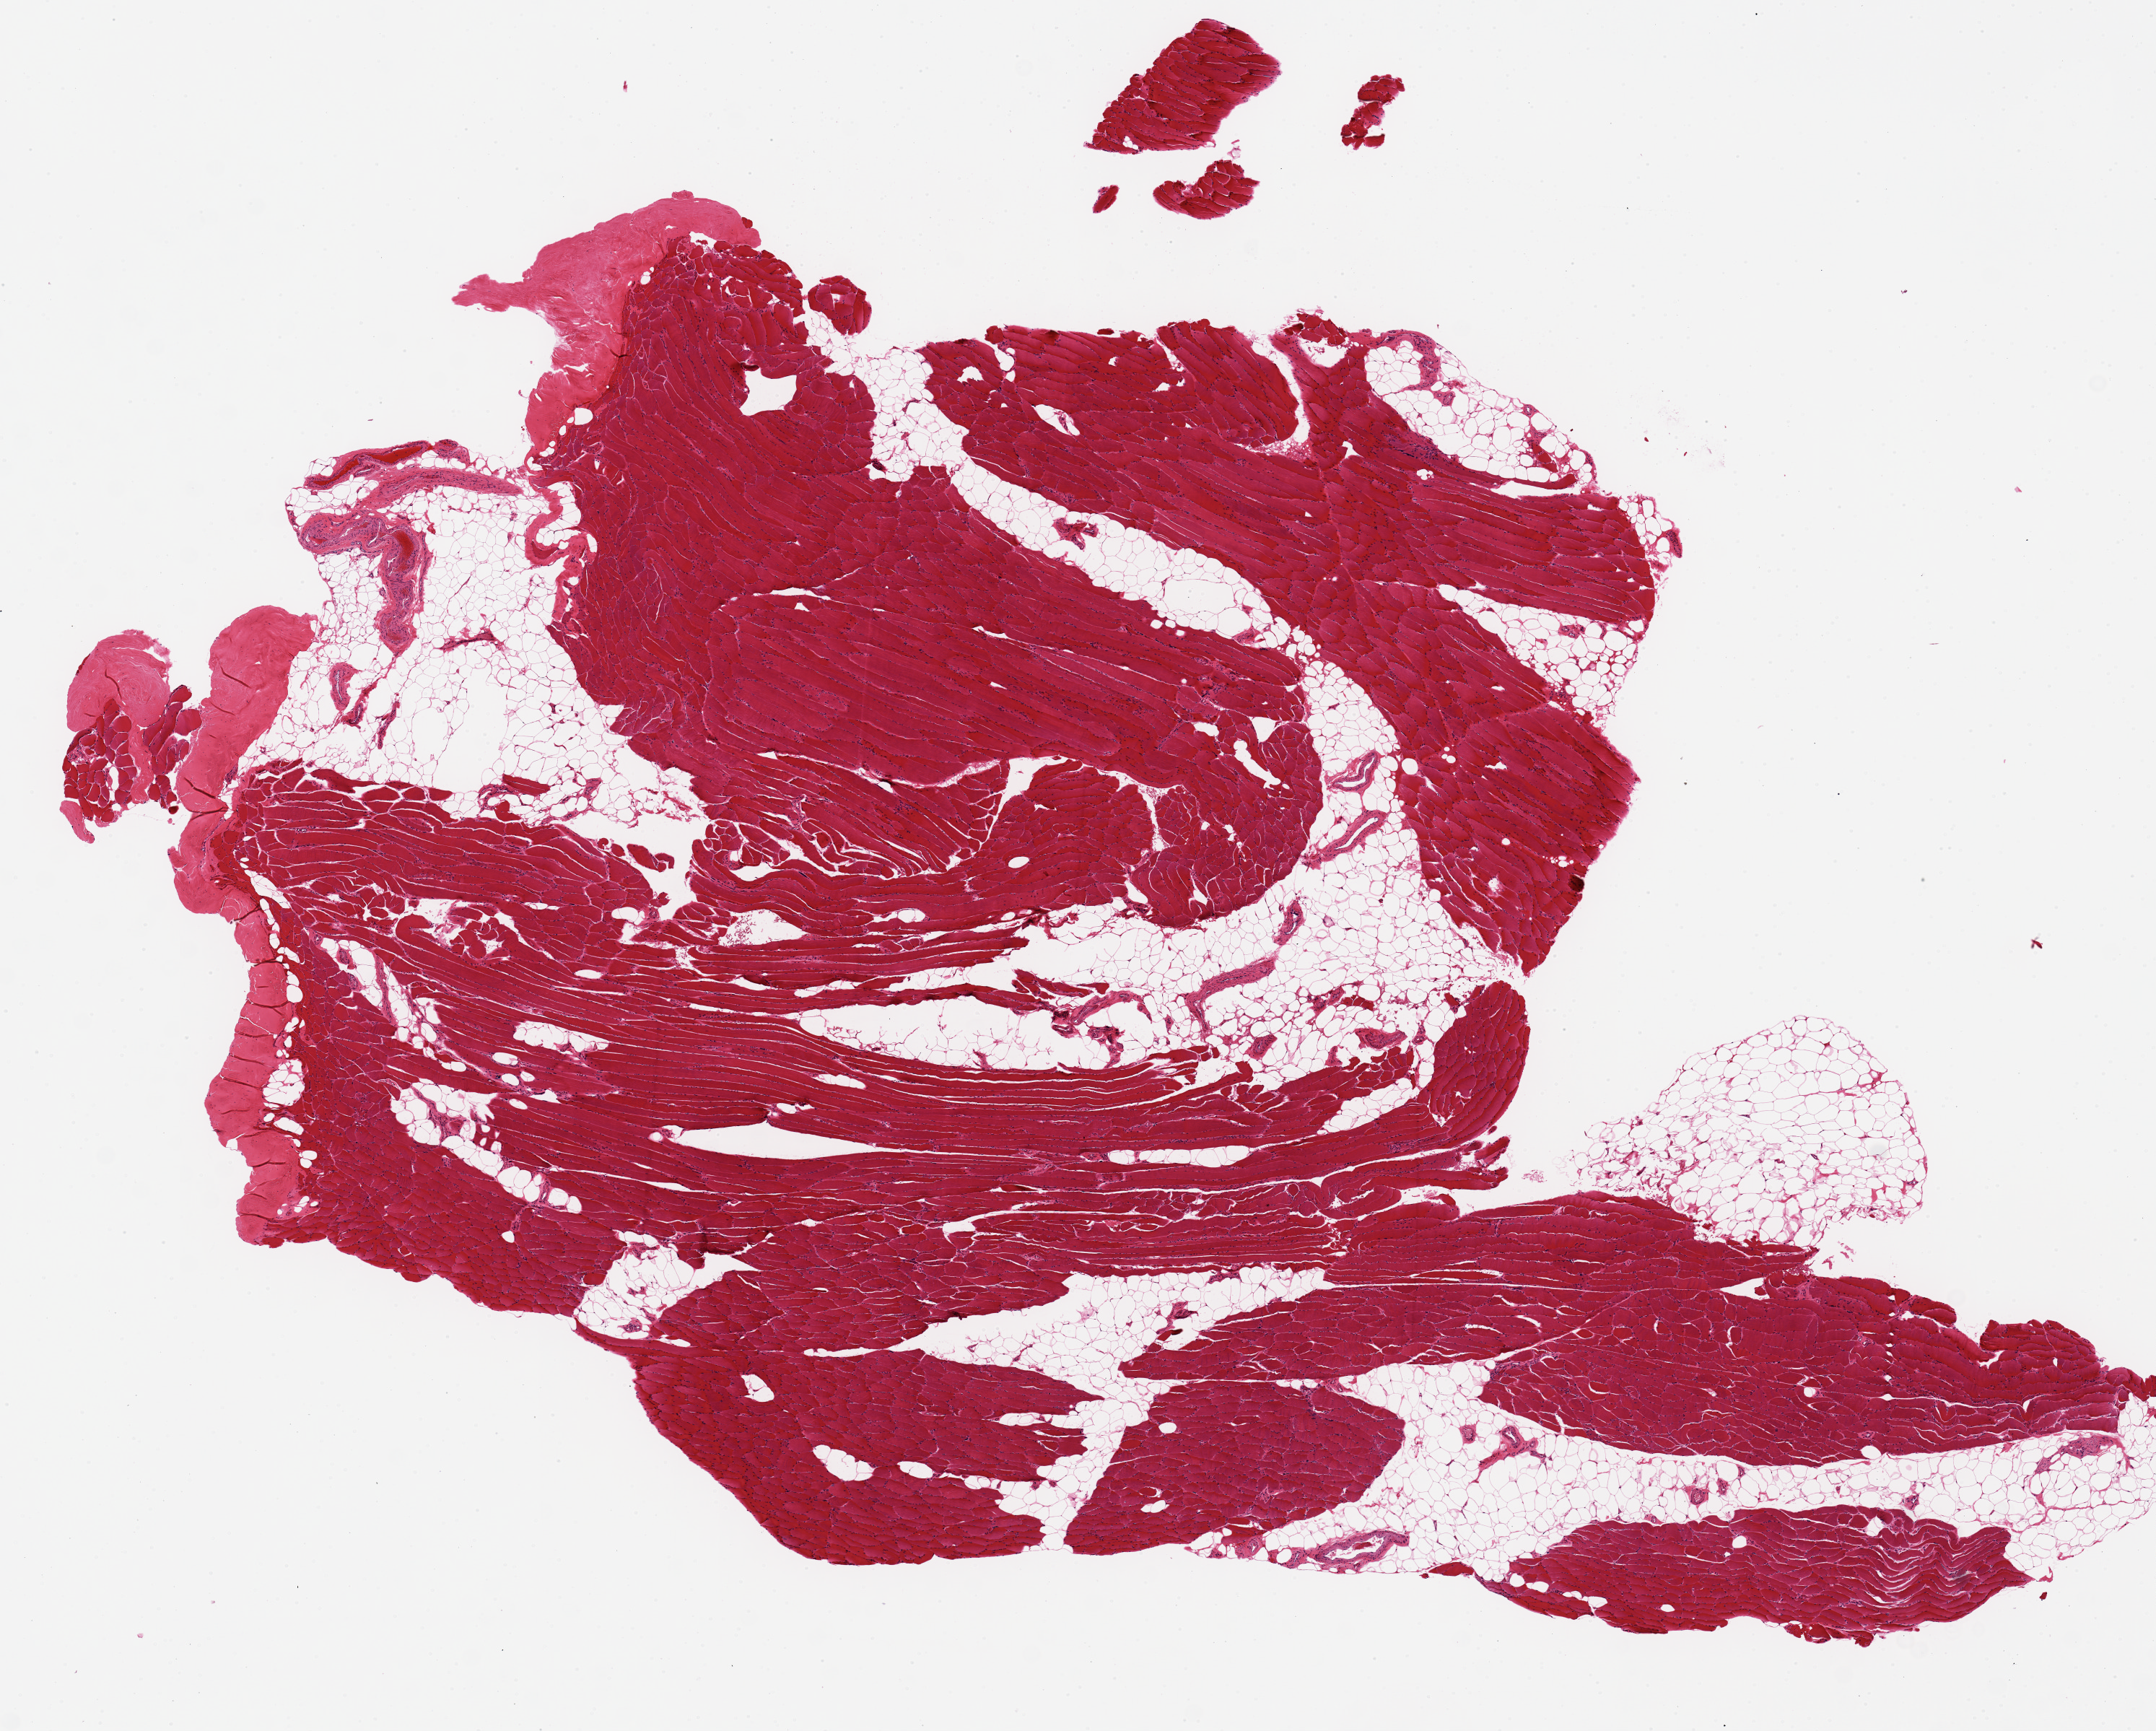
H&E whole-slide image — shown as a low-resolution overview of the whole scanned area (about 11.8 x 9.5 mm); PAXgene-fixed paraffin-embedded (PFPE) section; target tissue: skeletal muscle; donor tissue sample. Male donor.
Review note (as recorded): 30% fat.